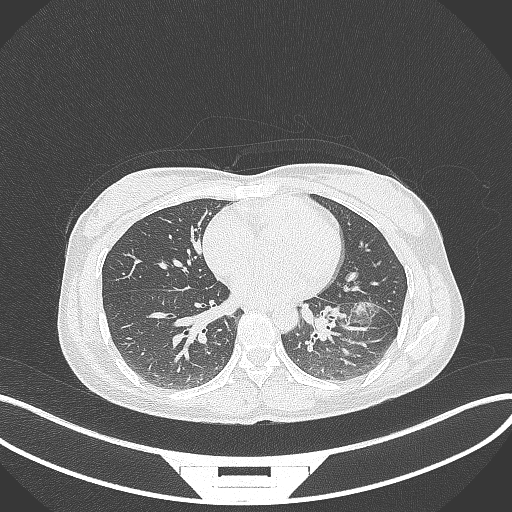
Chest CT, one axial slice. Position 37 of 244 along the scan axis. Reconstruction kernel B70f. 120 kVp. Lung window (W 1500 / L -600 HU). 1 mm slice thickness. 512 × 512 image matrix, field of view 400 × 400 mm. Female patient, age 41 years. From the clinical record (not read from this slice): clinical TNM (as recorded): T2a N3 M1b.
Outlined on this slice (rectangle marked by the reading radiologist):
- lung tumour (recorded histology: adenocarcinoma): bounding box <351,296,383,322> (left, top, right, bottom; pixels)